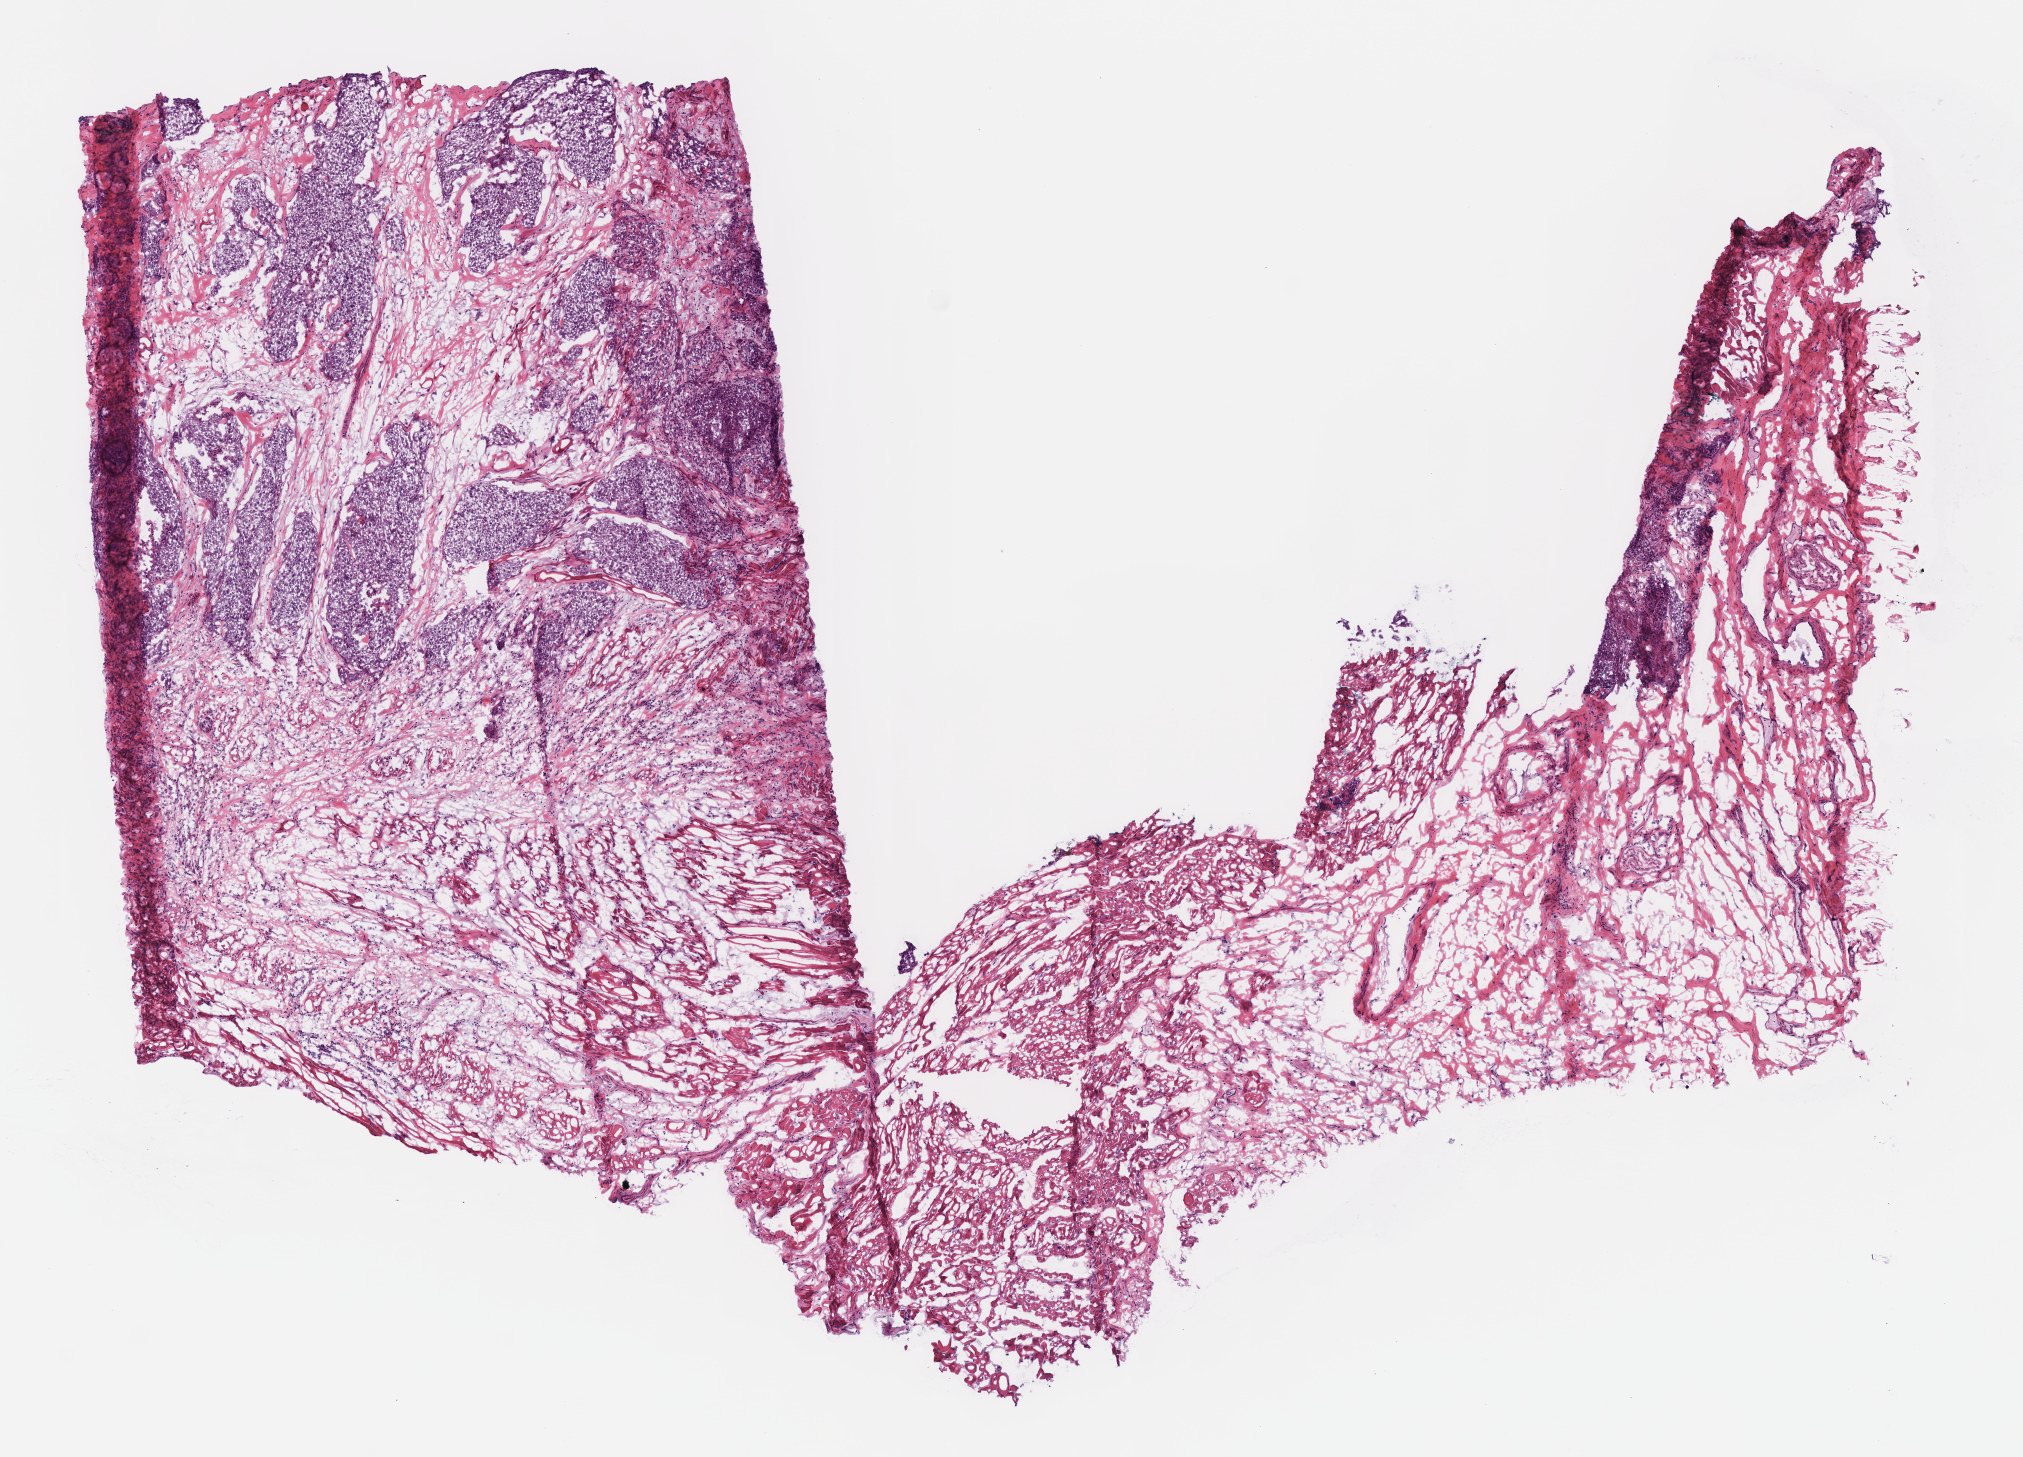
Hematoxylin and eosin (H&E) stained whole-slide image, shown as a low-resolution overview of the whole scanned area (about 8.0 x 5.7 mm, slide scanned at 40x), frozen section from the bottom of the tissue portion, head and neck, primary tumour sample. Male patient; age at initial diagnosis 49 years. Histologic grade: GX (grade cannot be assessed). Composition of this section per pathologist review: tumour cells 30%, tumour nuclei 55%, normal cells 20%, stromal cells 50%, necrosis 0%. Inflammatory infiltration, as recorded: lymphocyte infiltration 5%, monocyte infiltration 0%, neutrophil infiltration 0%.
AJCC pathologic stage: II (7th edition). Diagnosis: Squamous cell carcinoma, NOS (base of tongue, NOS).